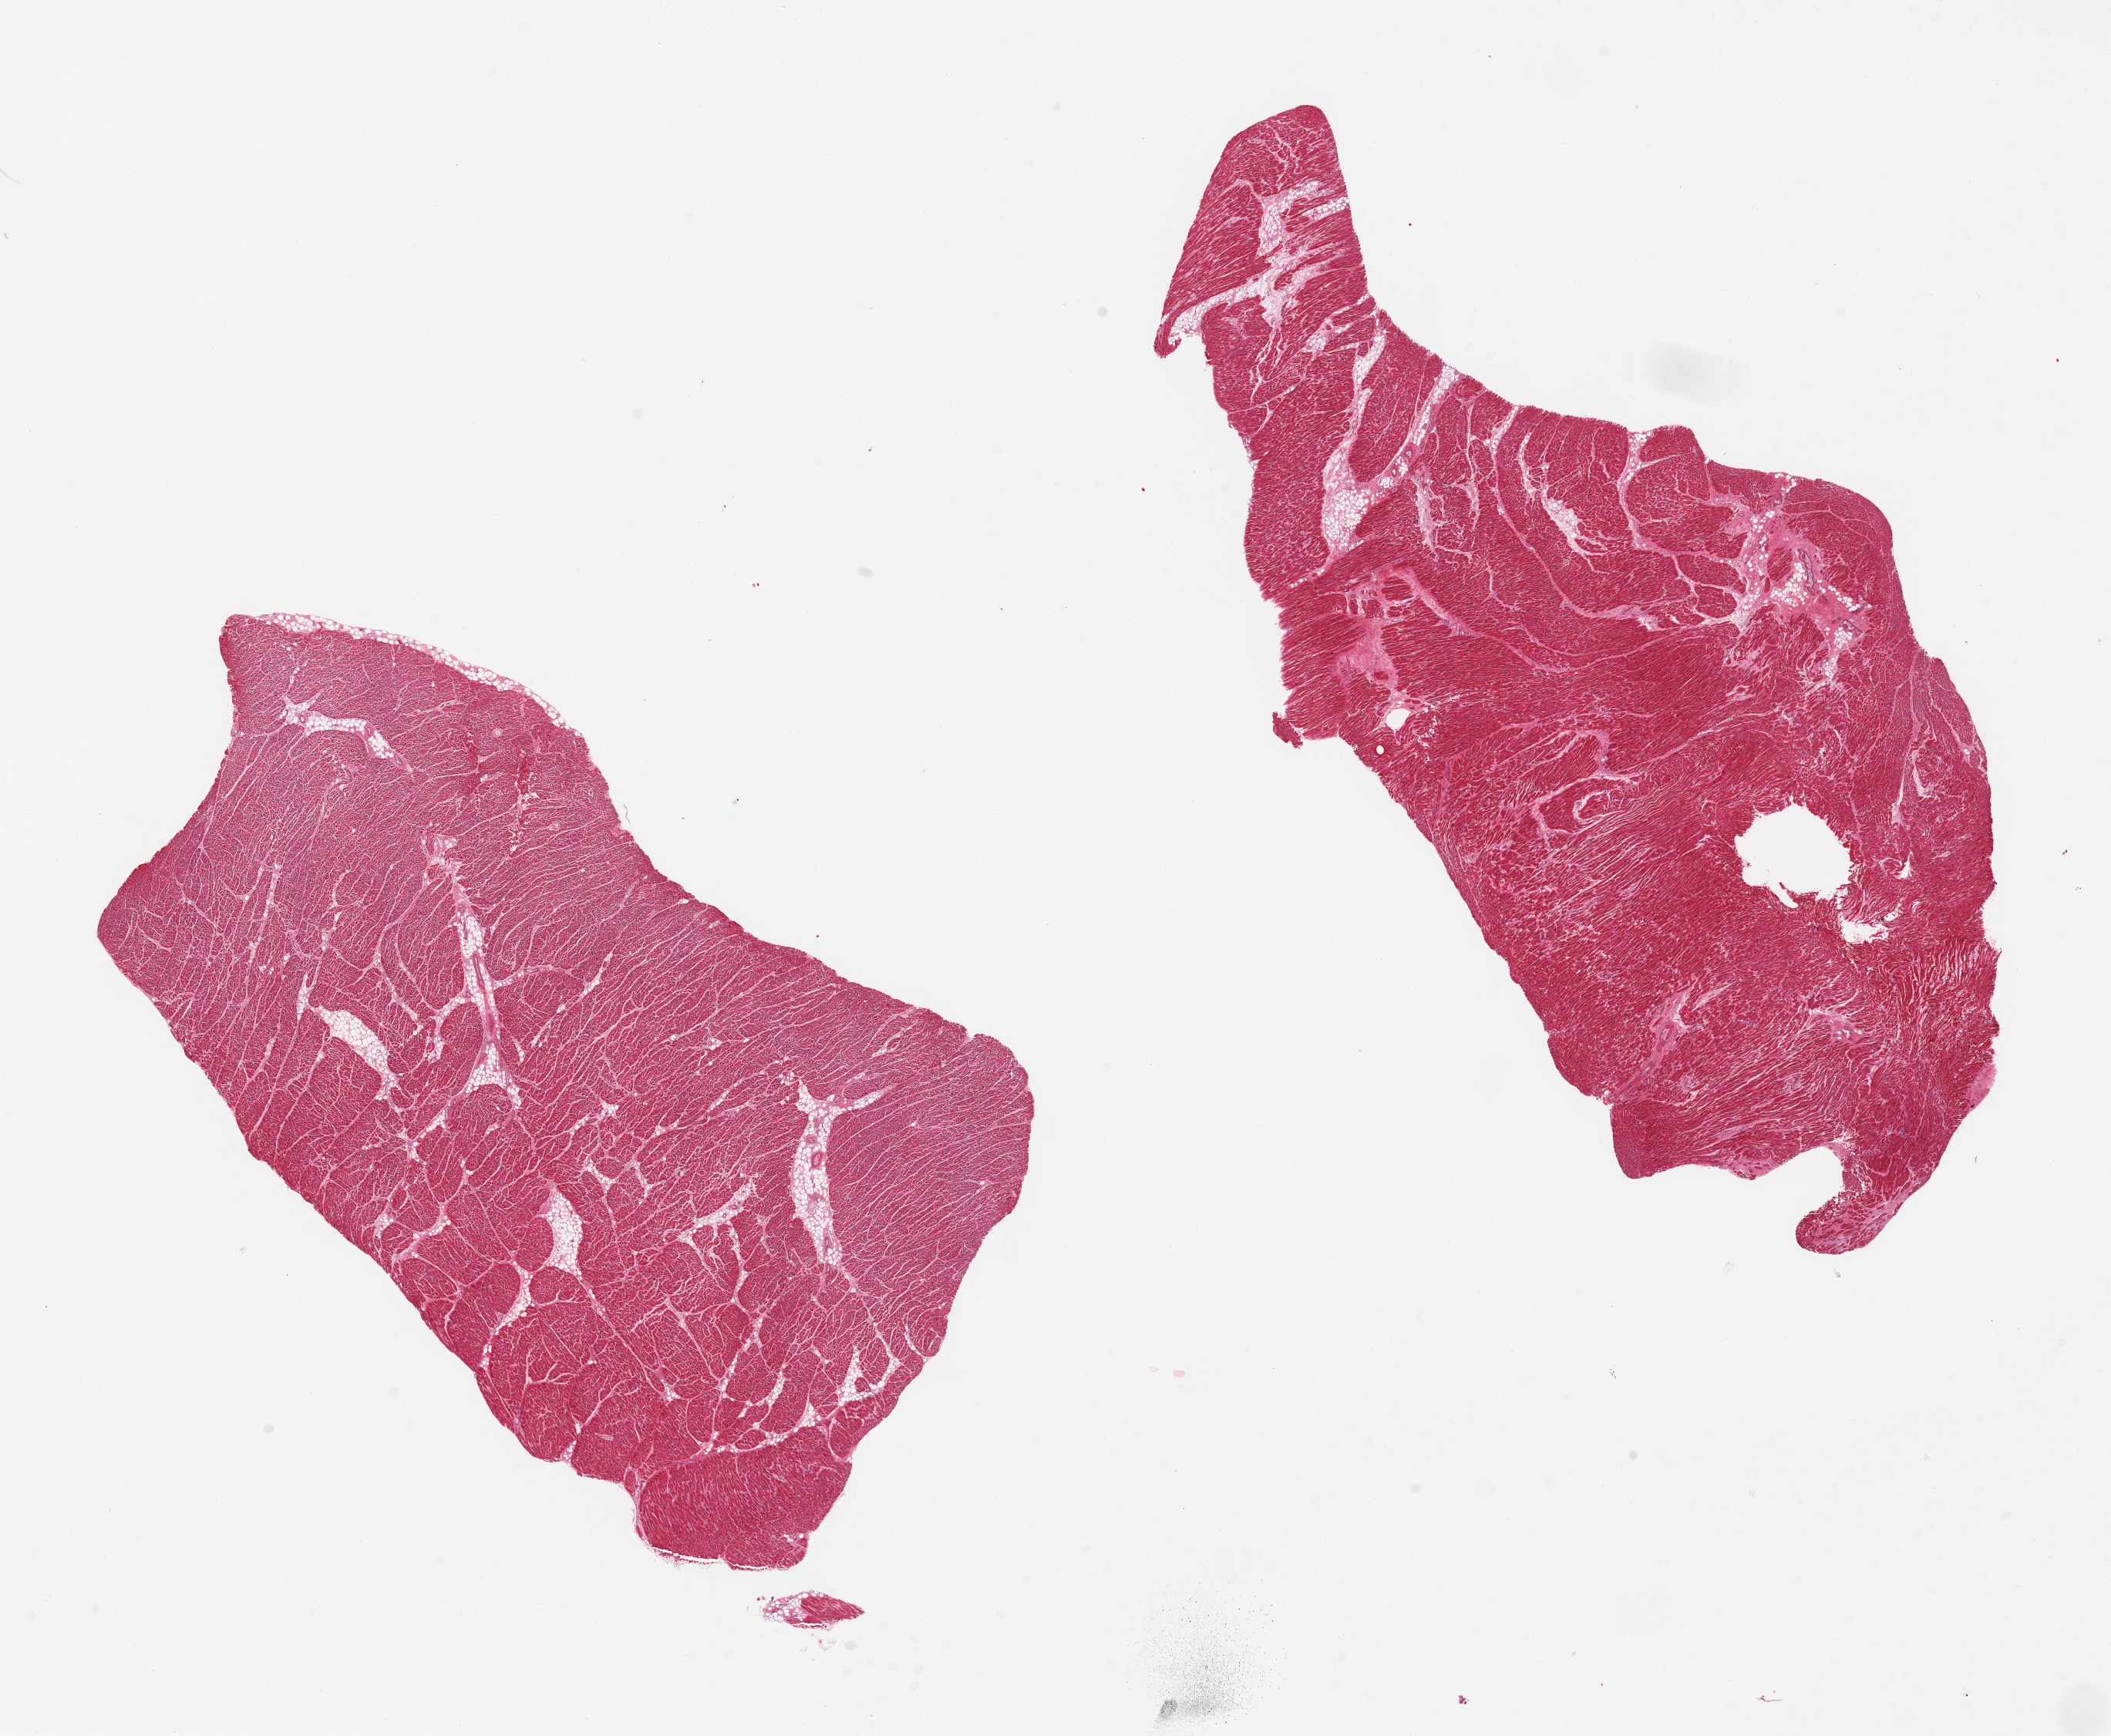
Hematoxylin and eosin (H&E) whole-slide image, brightfield — shown as a low-resolution overview of the whole scanned area (about 21.7 x 17.8 mm), PAXgene-fixed, paraffin-embedded tissue, section of heart (target tissue), tissue donor sample. Donor sex: female.
Pathologist's review note for this sample: 2 pieces; 5% internal fat; patchy hypereosinophilia (possible early ischemia).